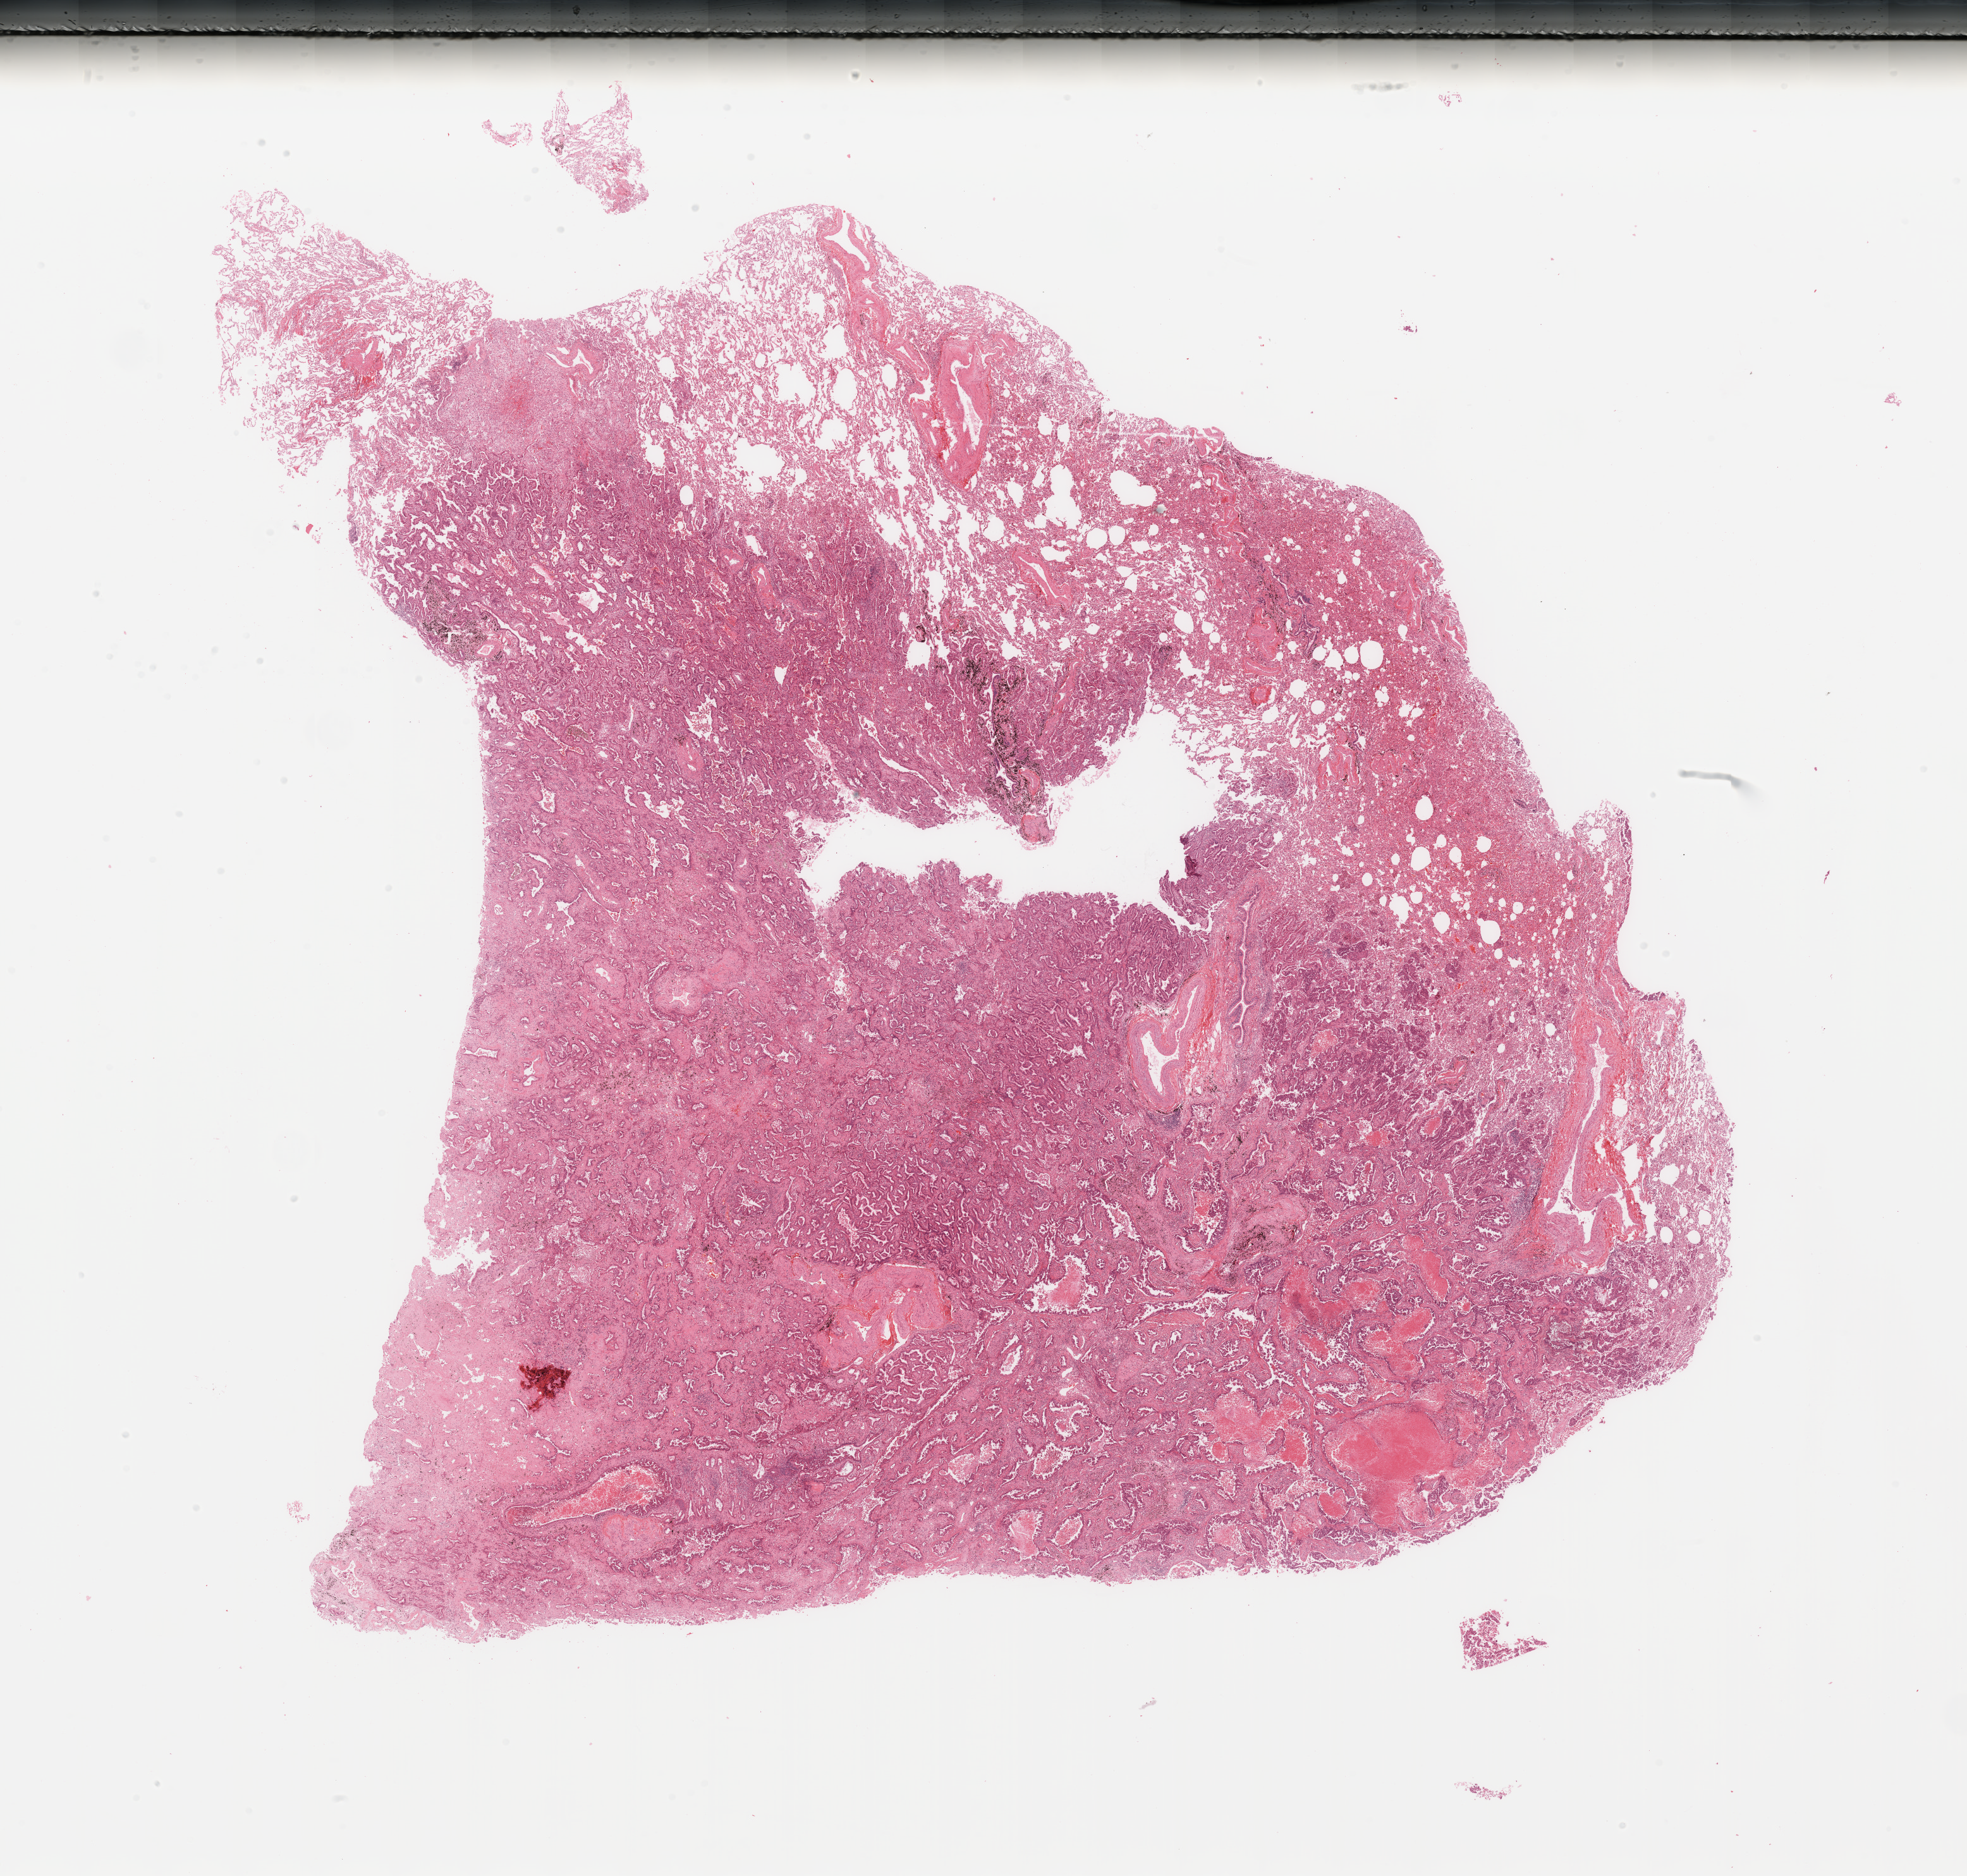
H&E whole-slide image — whole scanned area (about 24.6 x 23.5 mm, from a 20x scan) shown as a low-resolution overview. Tumour tissue sample, lung. 66-year-old female patient.
Diagnosis: Adenocarcinoma, NOS.